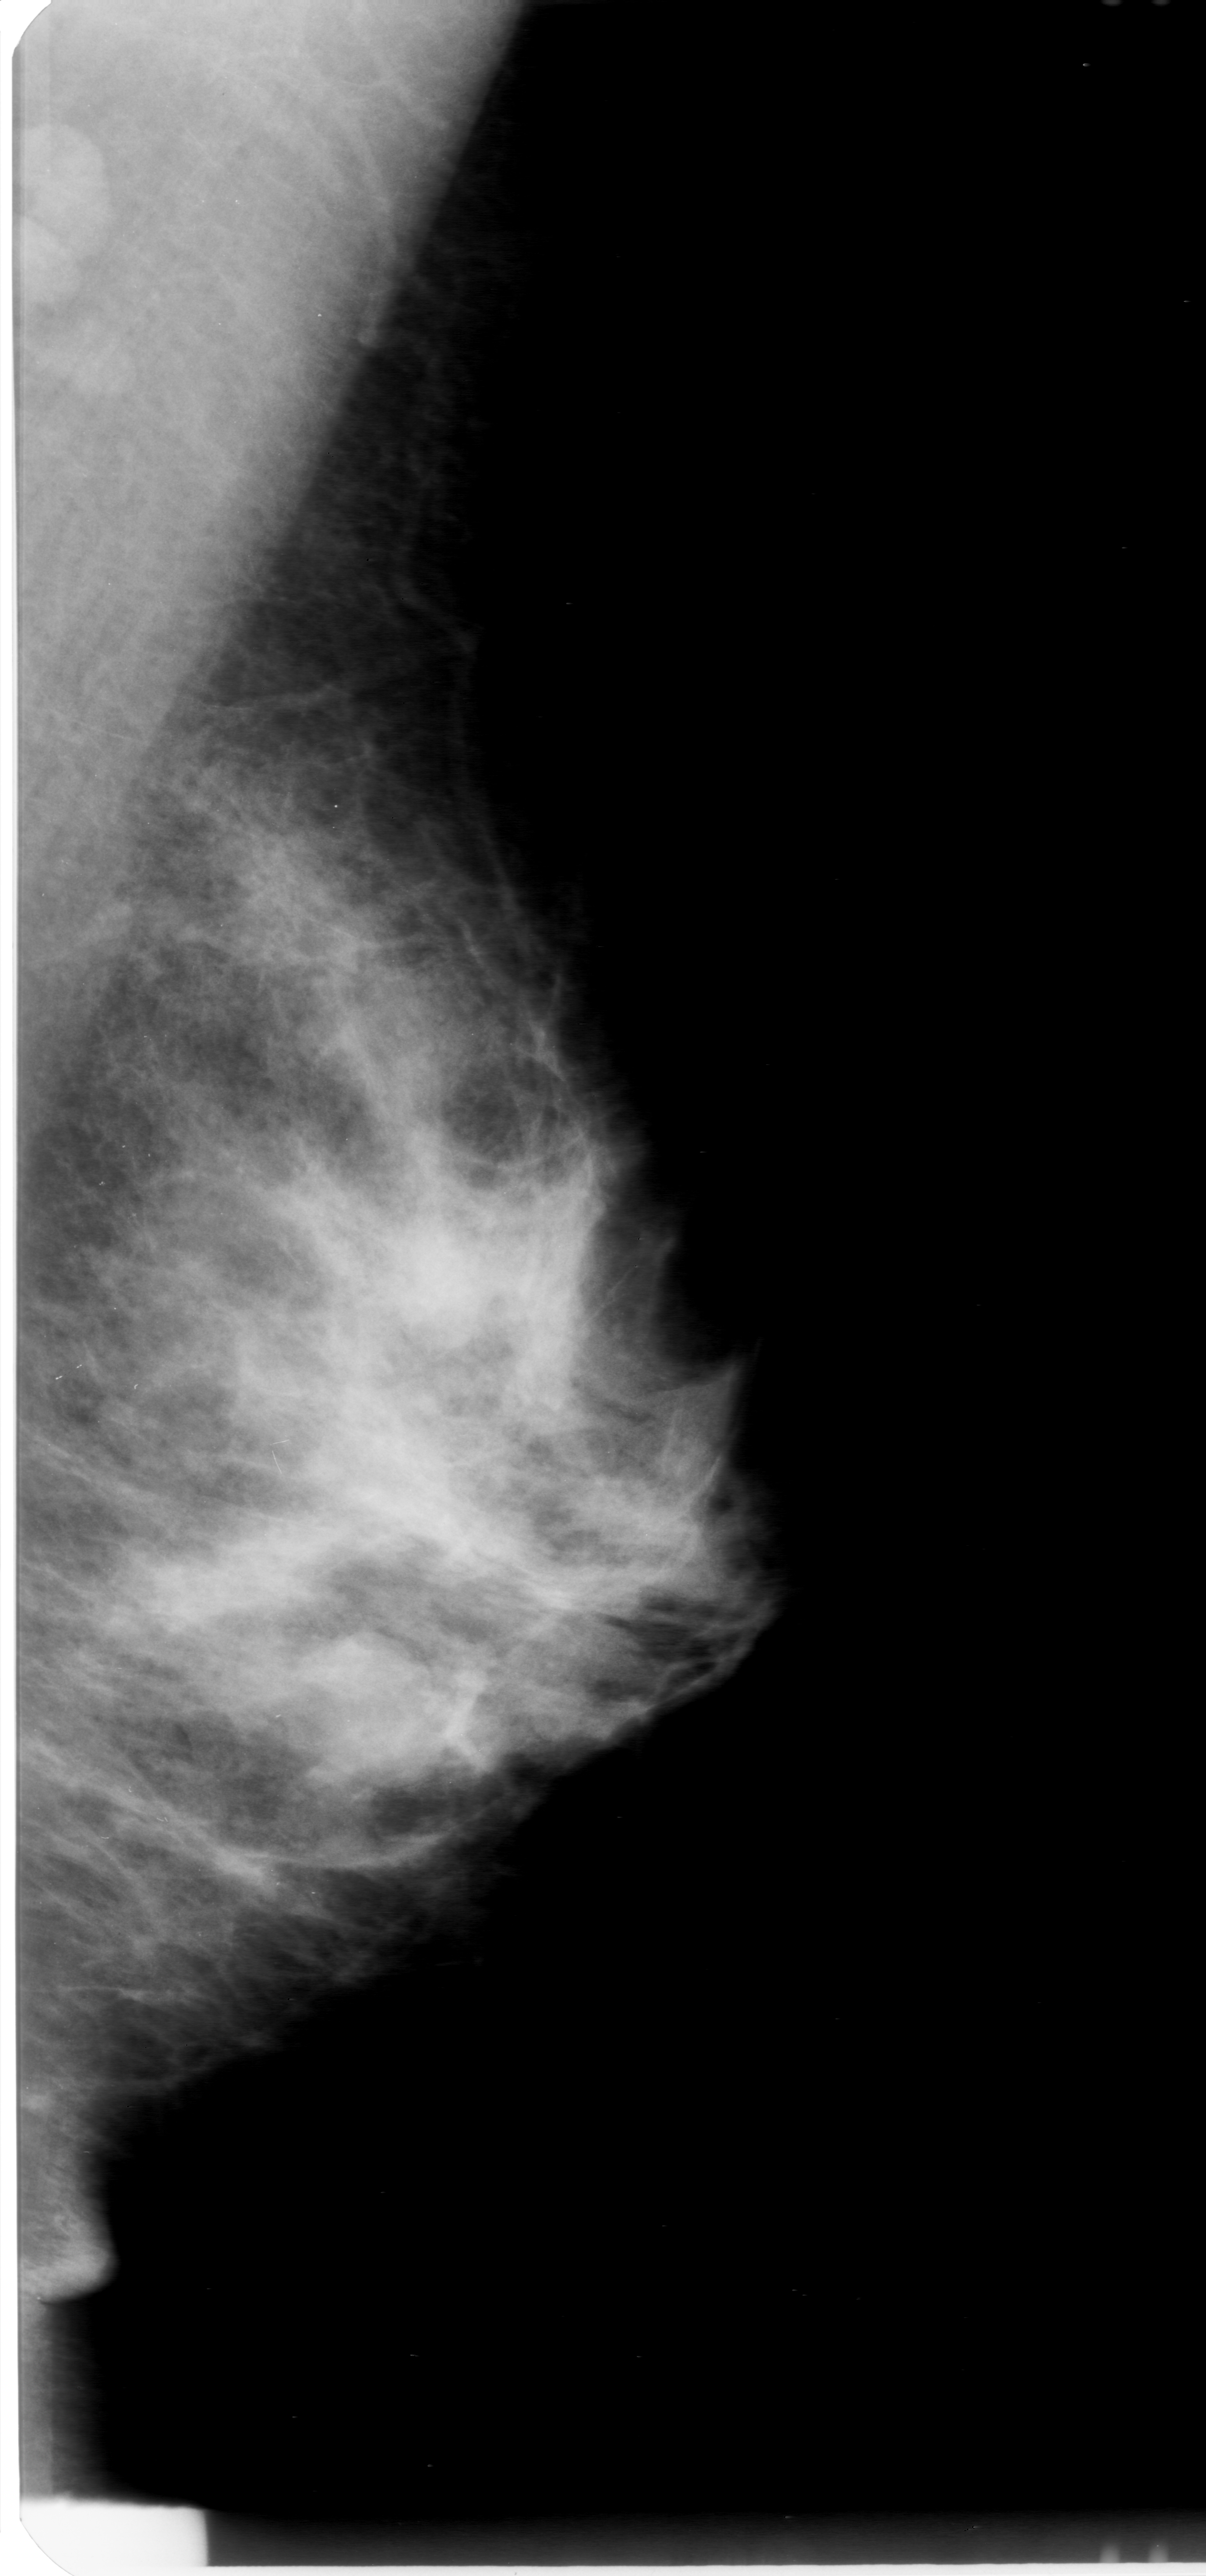
Digitized screen-film mammogram, left breast, MLO view.
Mass, shape lobulated, margins obscured; BI-RADS assessment category 0 (incomplete: needs additional imaging); pathology (as recorded): benign.